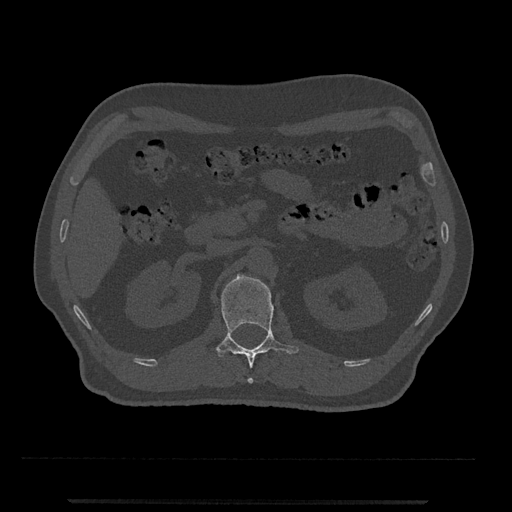
CT including the spine, one axial slice; position 333 of 797 along the scan axis; 120 kVp; bone window (W 1800 / L 400 HU); 0.5 mm slice thickness; 512 × 512 image matrix. Patient: male, 63 years. Case-level facts recorded for this patient, not image findings: primary cancer: prostate.
Annotated regions visible in this slice (semi-automatically segmented with operator editing):
- L1 vertebra: box from (x=216, y=274) to (x=299, y=384) px